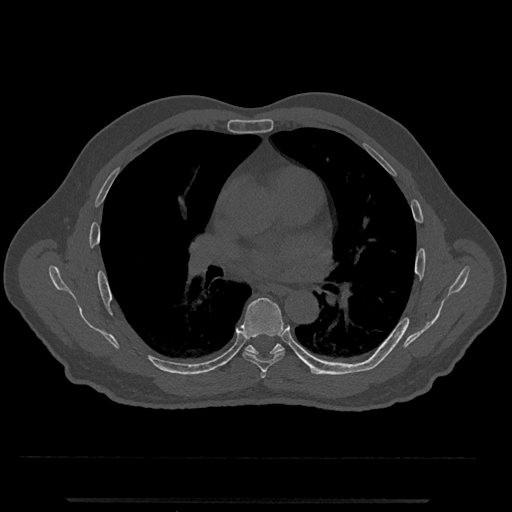
CT including the spine, one axial slice; position 720 of 797 along the scan axis; reconstruction kernel Br40s/3; 120 kVp; bone window (W 1800 / L 400 HU); 0.5 mm slice thickness; 512 × 512 image matrix, field of view 419 × 419 mm. Patient: male, 63 years. From the clinical record (not read from this slice): primary cancer: prostate.
Structures marked on this image (semi-automatically segmented with operator editing):
- T5 vertebra: bounding box <260,371,267,379> (left, top, right, bottom; pixels)
- T6 vertebra: <241,298,285,372>
- T7 vertebra: <245,343,328,375>